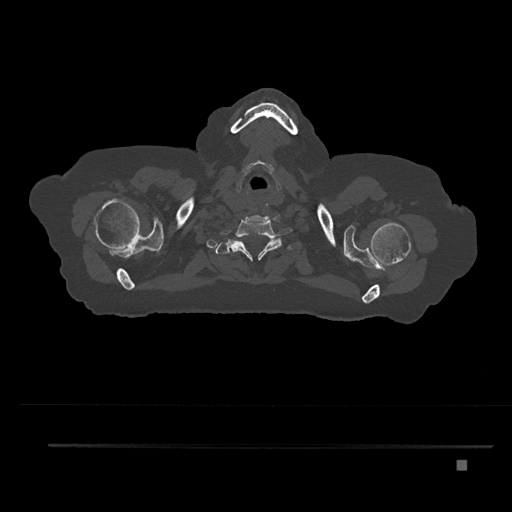
CT including the spine, one axial slice. Slice 718 of 797 in the series (ordered by position). 120 kVp. Bone window (W 1800 / L 400 HU). 0.5 mm slice thickness. 512 × 512 image matrix, field of view 437 × 437 mm. Patient: female, 76 years. Case-level facts recorded for this patient, not image findings: primary cancer: lung; vertebrae with lytic lesions (as recorded): T11, L3.
Structures marked on this image (semi-automatic segmentation, software-assisted and operator-edited):
- T1 vertebra: bounding box <221,241,266,259> (left, top, right, bottom; pixels)